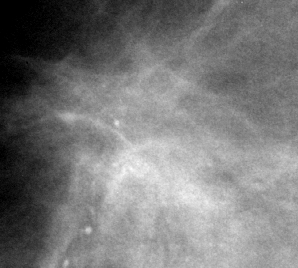
Cropped region of a digitized screen-film mammogram centred on a radiologist-marked abnormality; right breast; MLO view.
- Finding: mass, shape architectural distortion, margins ill defined / spiculated; BI-RADS assessment category 4; pathology result (as recorded, not read from the image): malignant.